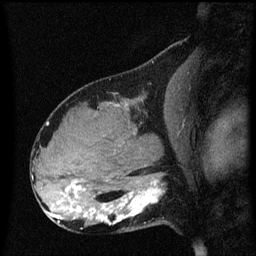
Breast MRI (dynamic contrast-enhanced), one sagittal slice; position 29 of 60 along the scan axis; dynamic contrast-enhanced series, image 2 of 3 at this slice position (ordered by acquisition); 1.5 T; TE 4.2 ms, TR 8.4 ms; 256 × 256 image matrix. Patient: female, 31 years. From the clinical record (not read from this slice): setting: breast cancer imaged before/during neoadjuvant chemotherapy; receptor status: HR-positive, HER2-negative.
Outlined on this slice (semi-automatically segmented with operator editing):
- analysis volume of interest (the breast-tissue region the enhancement analysis was run in; not a lesion): bounding box (x1, y1, x2, y2) in pixels: (102, 166, 169, 229)
- tumour enhancement mask (voxels above the 70 % enhancement threshold inside the analysis volume of interest): (102, 180, 161, 223)